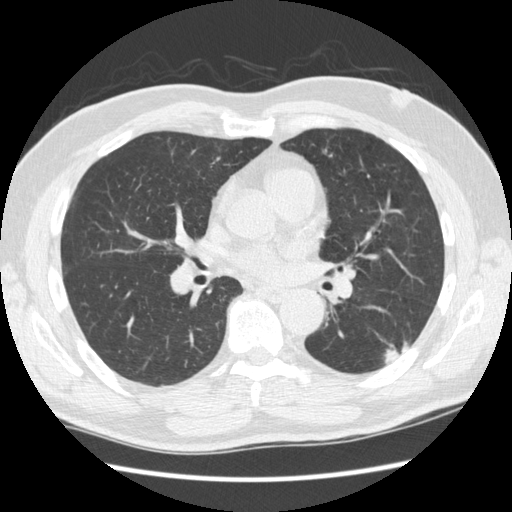
Axial slice from a low-dose chest CT screening exam. Baseline annual screen. Lung window (W 1500 / L -600 HU). 1.25 mm slice thickness. Standard (soft-tissue) reconstruction kernel (STANDARD). Slice 124 of 267 in the series. Male participant, aged 74 years at enrolment. Former smoker at enrolment.
Expert reader's lesion annotation, bounding box (x1, y1, x2, y2) in pixels: (373, 324, 415, 370). The screening reader recorded 3 non-calcified nodules or masses ≥4 mm on this exam (right upper lobe, right lower lobe, left upper lobe); which of them this box marks is not recorded. Official screen result: positive, change unspecified: nodule(s) >= 4 mm or enlarging nodule(s), mass(es), or other non-specific abnormalities suspicious for lung cancer. Lung cancer was diagnosed 384 days after this screen: squamous cell carcinoma, NOS, left lower lobe, well differentiated (G1), stage IA (AJCC 6th edition), 28 mm at pathology.